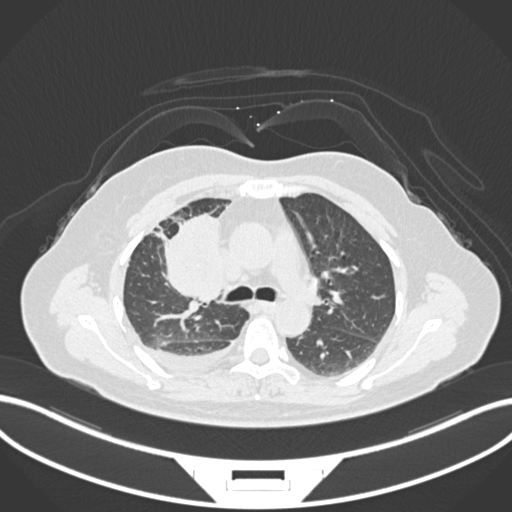
Chest CT, one axial slice; slice 97 of 172 in the series (ordered by position); reconstruction kernel B30f; 120 kVp; lung window (W 1500 / L -600 HU); 1 mm slice thickness; 512 × 512 image matrix, field of view 400 × 400 mm. Patient: female, 52 years. Case-level facts recorded for this patient, not image findings: clinical TNM (as recorded): T3 N1 M1.
Annotated regions visible in this slice (bounding box drawn by a radiologist):
- lung tumour (recorded histology: adenocarcinoma): bounding box [x1, y1, x2, y2] px = [152, 211, 224, 307]